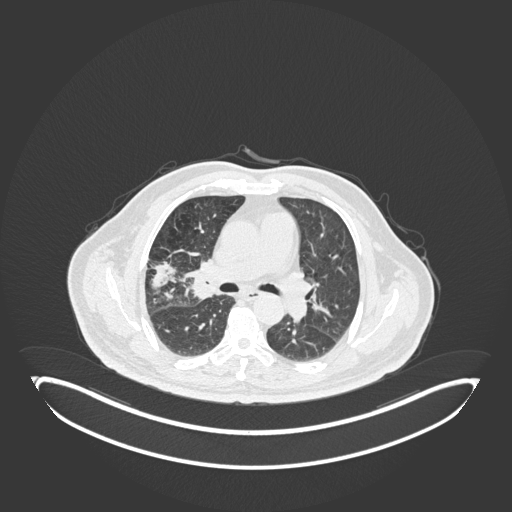
Chest CT, one axial slice. Reconstruction kernel B30f. 120 kVp. Lung window (W 1500 / L -600 HU). 512 × 512 image matrix, field of view 500 × 500 mm. Male patient, age 72 years. Case-level facts recorded for this patient, not image findings: clinical TNM (as recorded): T1c N0 M0; histopathological grade: G2.
Annotated regions visible in this slice (bounding box drawn by a radiologist):
- lung tumour (recorded histology: squamous cell carcinoma): box from (x=181, y=250) to (x=213, y=311) px